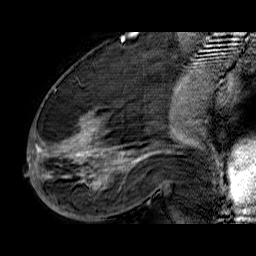
Breast MRI (dynamic contrast-enhanced), one sagittal slice; position 28 of 60 along the scan axis; dynamic contrast-enhanced series, time point 2 of 6 at this slice position (early post-contrast); 1.5 T; TE 6.5 ms, TR 32.9 ms; 4 mm slice thickness; 256 × 256 image matrix, field of view 200 × 200 mm. Female patient. From the clinical record (not read from this slice): setting: breast cancer imaged before/during neoadjuvant chemotherapy; receptor status: HR-positive, HER2-negative.
Outlined on this slice (semi-automatically segmented with operator editing):
- analysis volume of interest (the breast-tissue region the enhancement analysis was run in; not a lesion): bounding box (x1, y1, x2, y2) in pixels: (33, 74, 176, 210)
- tumour enhancement mask (voxels above the 100 % enhancement threshold inside the analysis volume of interest): (33, 113, 165, 189)